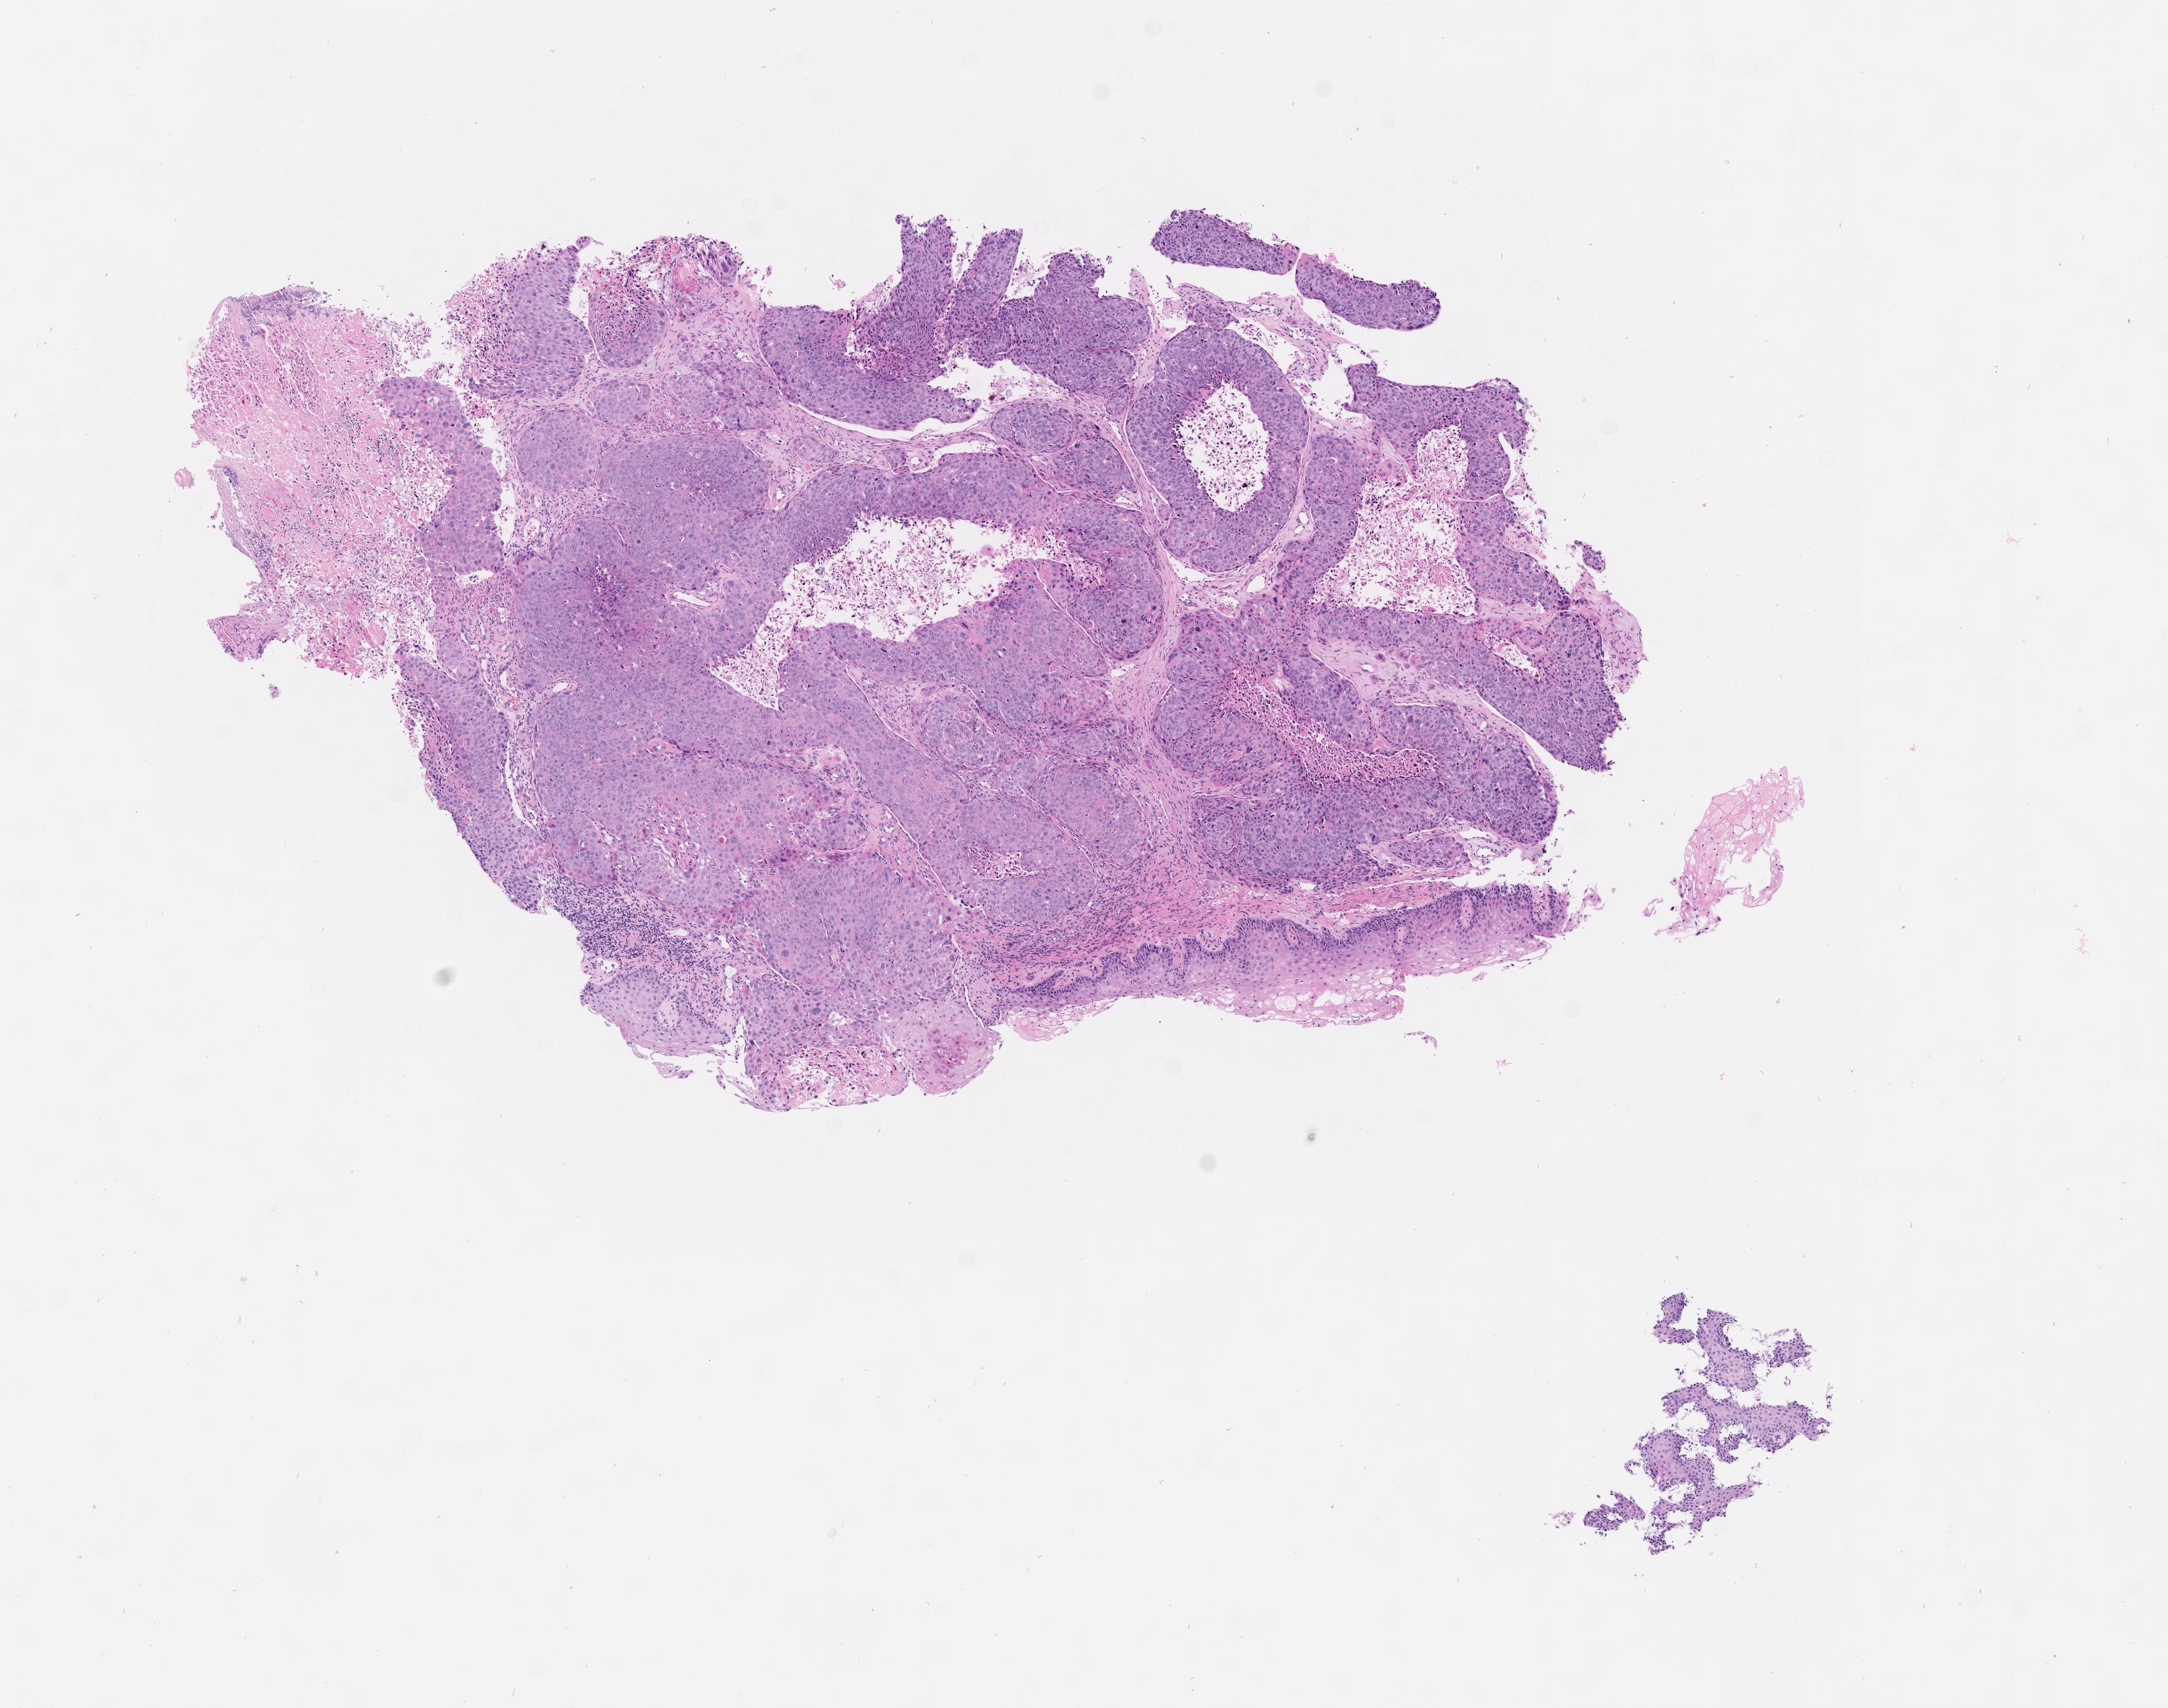
Digitized hematoxylin and eosin (H&E)-stained section — shown as a low-resolution overview of the whole scanned area (about 7.0 x 5.6 mm), specimen: tumor tissue, anatomic site: cervix. Female patient, 32 years old.
Histologic diagnosis: Squamous cell carcinoma, keratinizing, NOS.